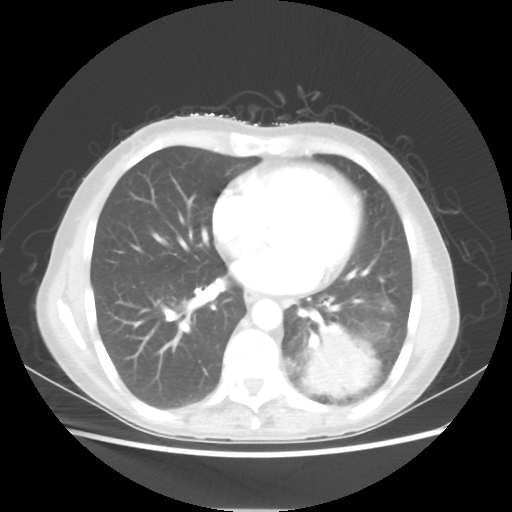
Chest CT, one axial slice; slice 23 of 56 in the series (ordered by position); lung window (W 1500 / L -600 HU); 512 × 512 image matrix, field of view 360 × 360 mm. Patient: female, 53 years. From the clinical record (not read from this slice): clinical TNM (as recorded): T3 N0 M0.
Structures marked on this image (bounding box drawn by a radiologist):
- lung tumour (recorded histology: adenocarcinoma): bounding box (x1, y1, x2, y2) in pixels: (302, 328, 377, 399)